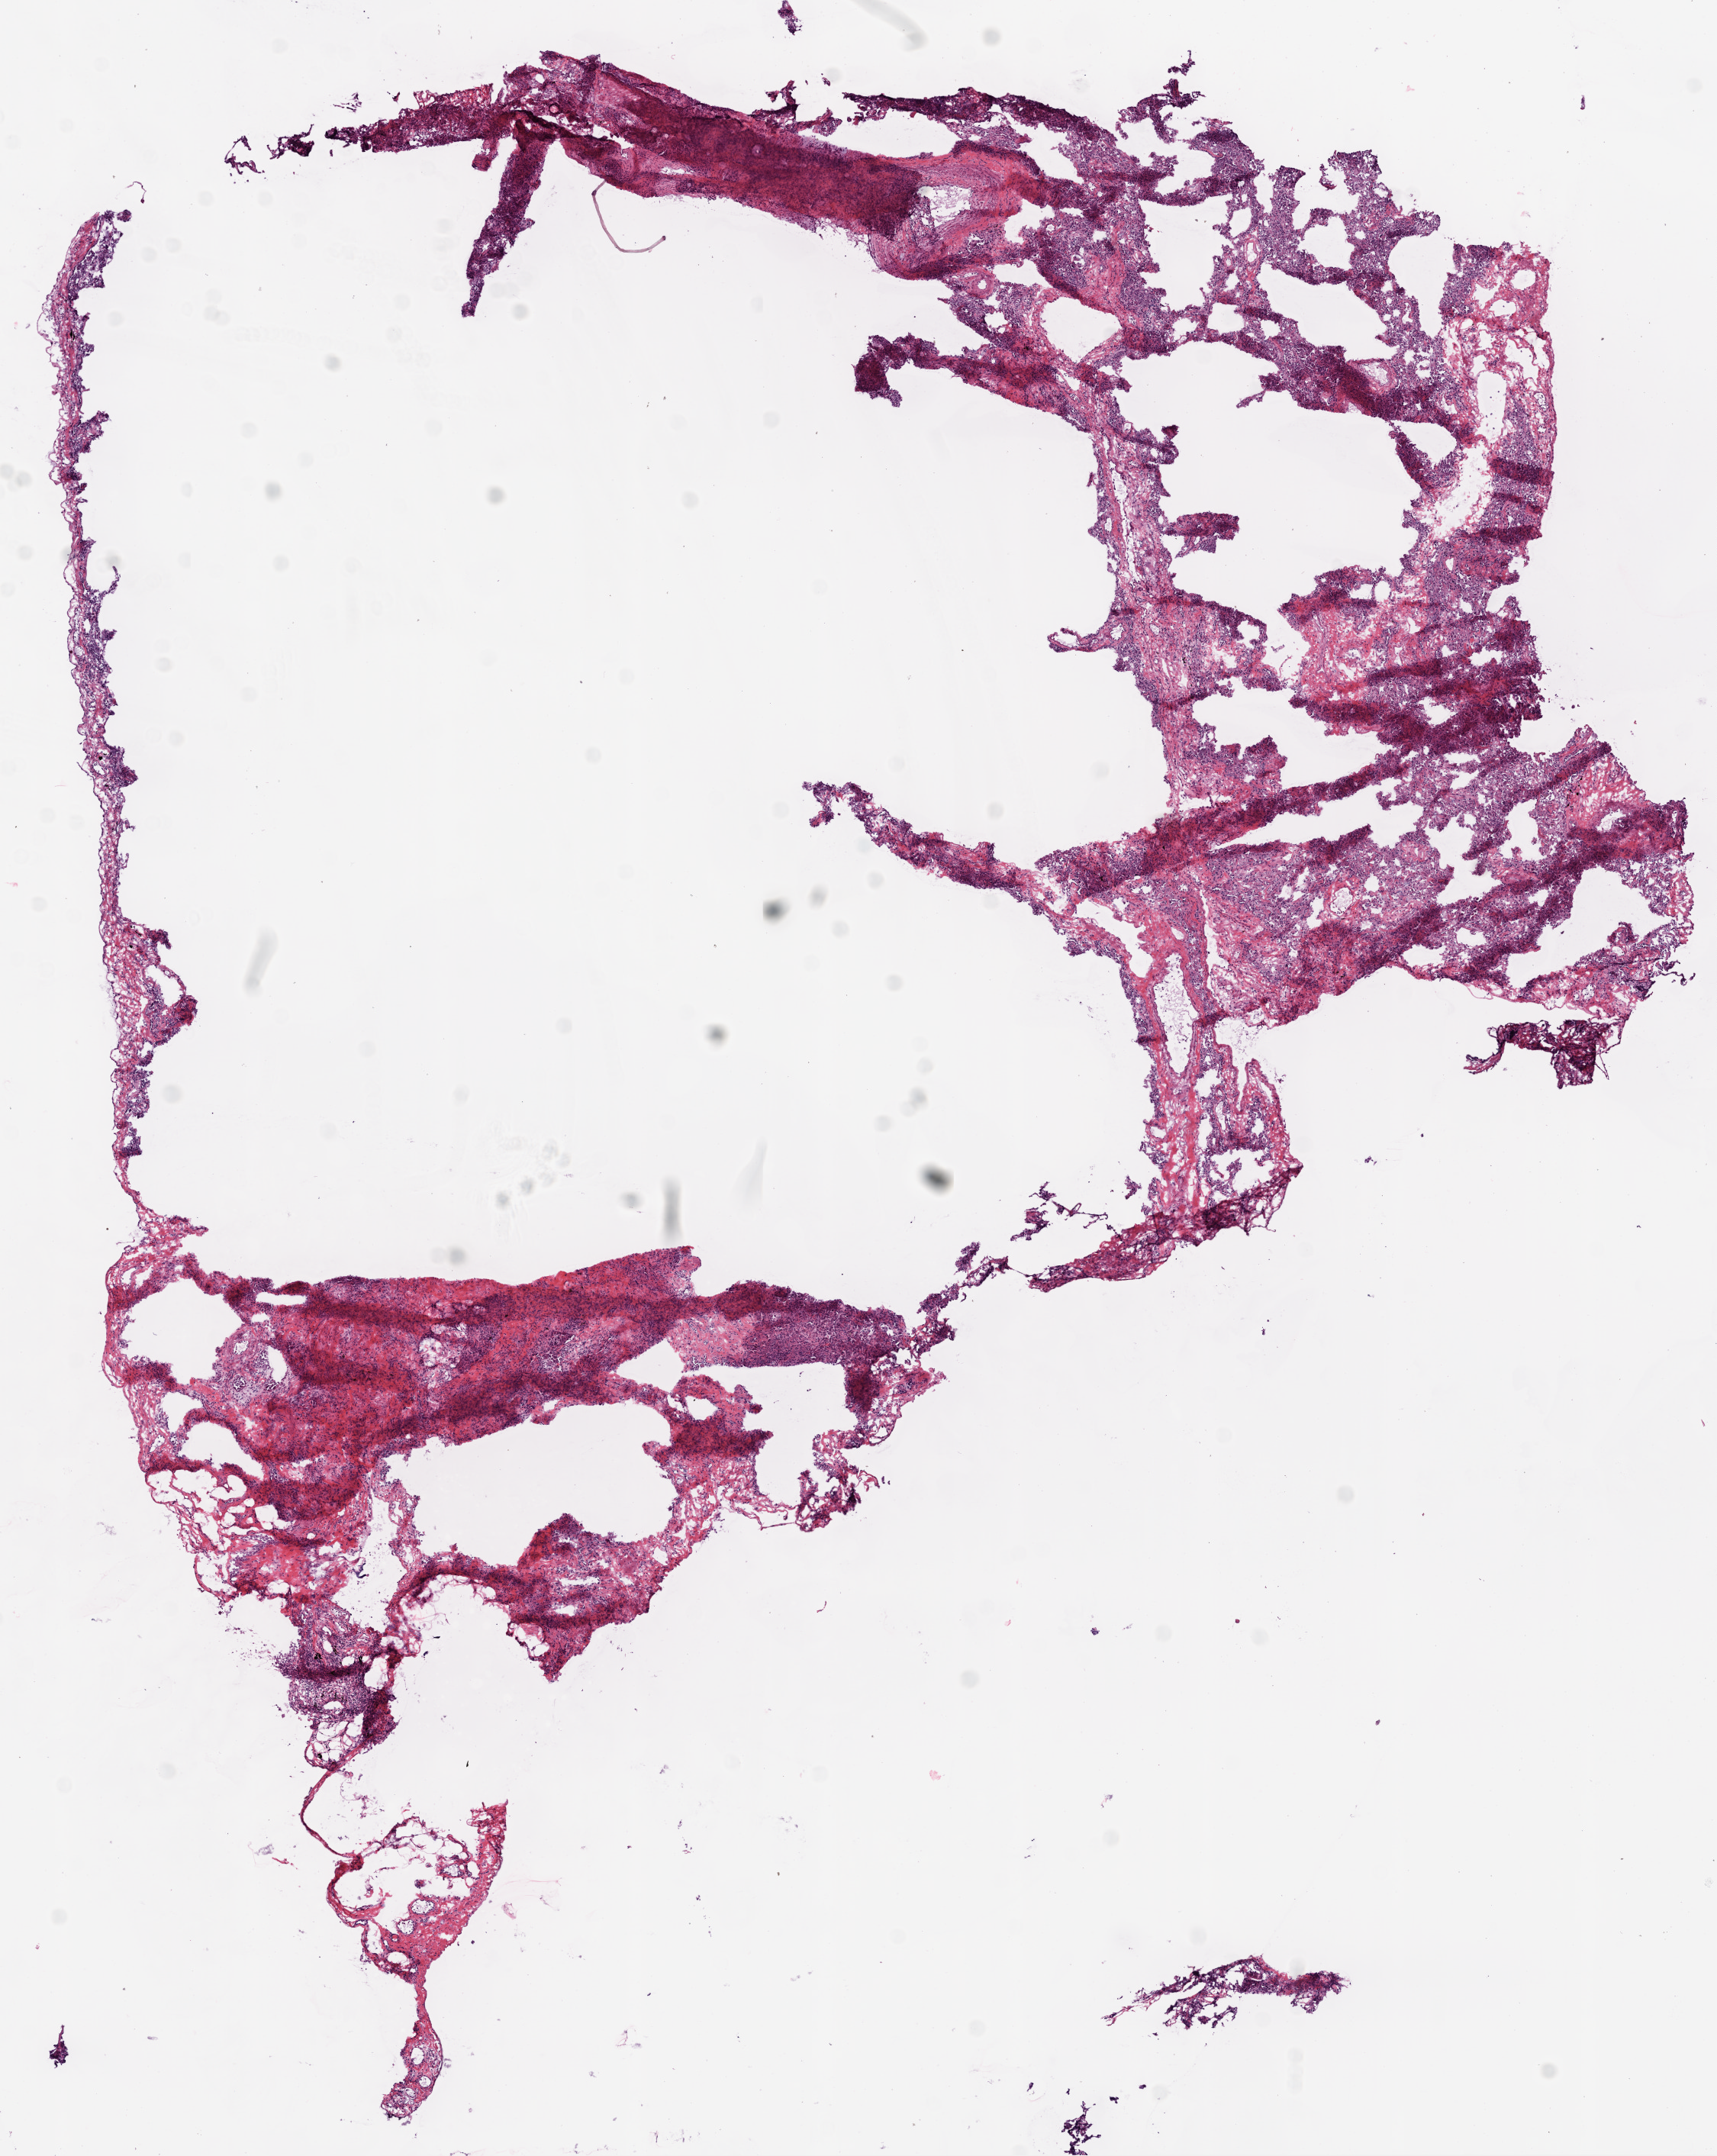
Whole-slide histology image, H&E, whole scanned area (about 9.0 x 11.3 mm, from a 20x scan) shown as a low-resolution overview. Frozen section. Solid tissue normal (non-tumour tissue) sample from the lung. Patient: male, age at initial diagnosis 69 years.
* this section: solid tissue normal sample (biorepository sample class)
* patient diagnosis: Squamous cell carcinoma, NOS (lower lobe, lung)